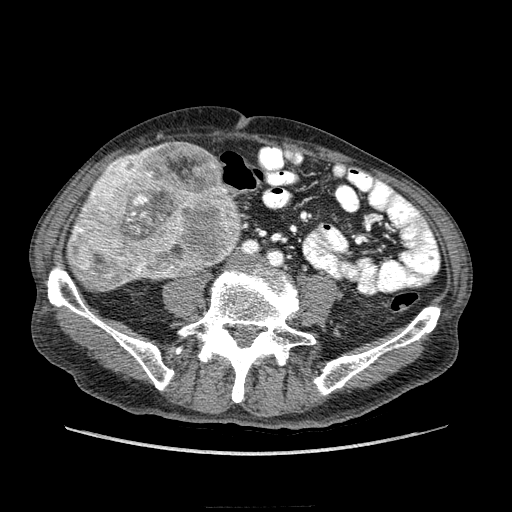
Contrast-enhanced abdominal CT (liver protocol), one axial slice. Position 37 of 218 along the scan axis. Reconstruction kernel STANDARD. Soft-tissue window (W 400 / L 40 HU). 2.5 mm slice thickness. 512 × 512 image matrix, field of view 380 × 380 mm. From the clinical record (not read from this slice): diagnosis: hepatocellular carcinoma (patient treated with transarterial chemoembolisation; whether this scan precedes or follows treatment is not stated here); TNM stage (as recorded): Stage-IIIA; Child-Pugh class: A; tumour nodularity: multinodular.
Annotated regions visible in this slice (semi-automatic segmentation, software-assisted and operator-edited):
- liver parenchyma outside the tumour (the mass and vessels are separate outlines, so this box may not span the whole liver): bounding box <72,178,144,278> (left, top, right, bottom; pixels)
- mass: <66,141,243,292>